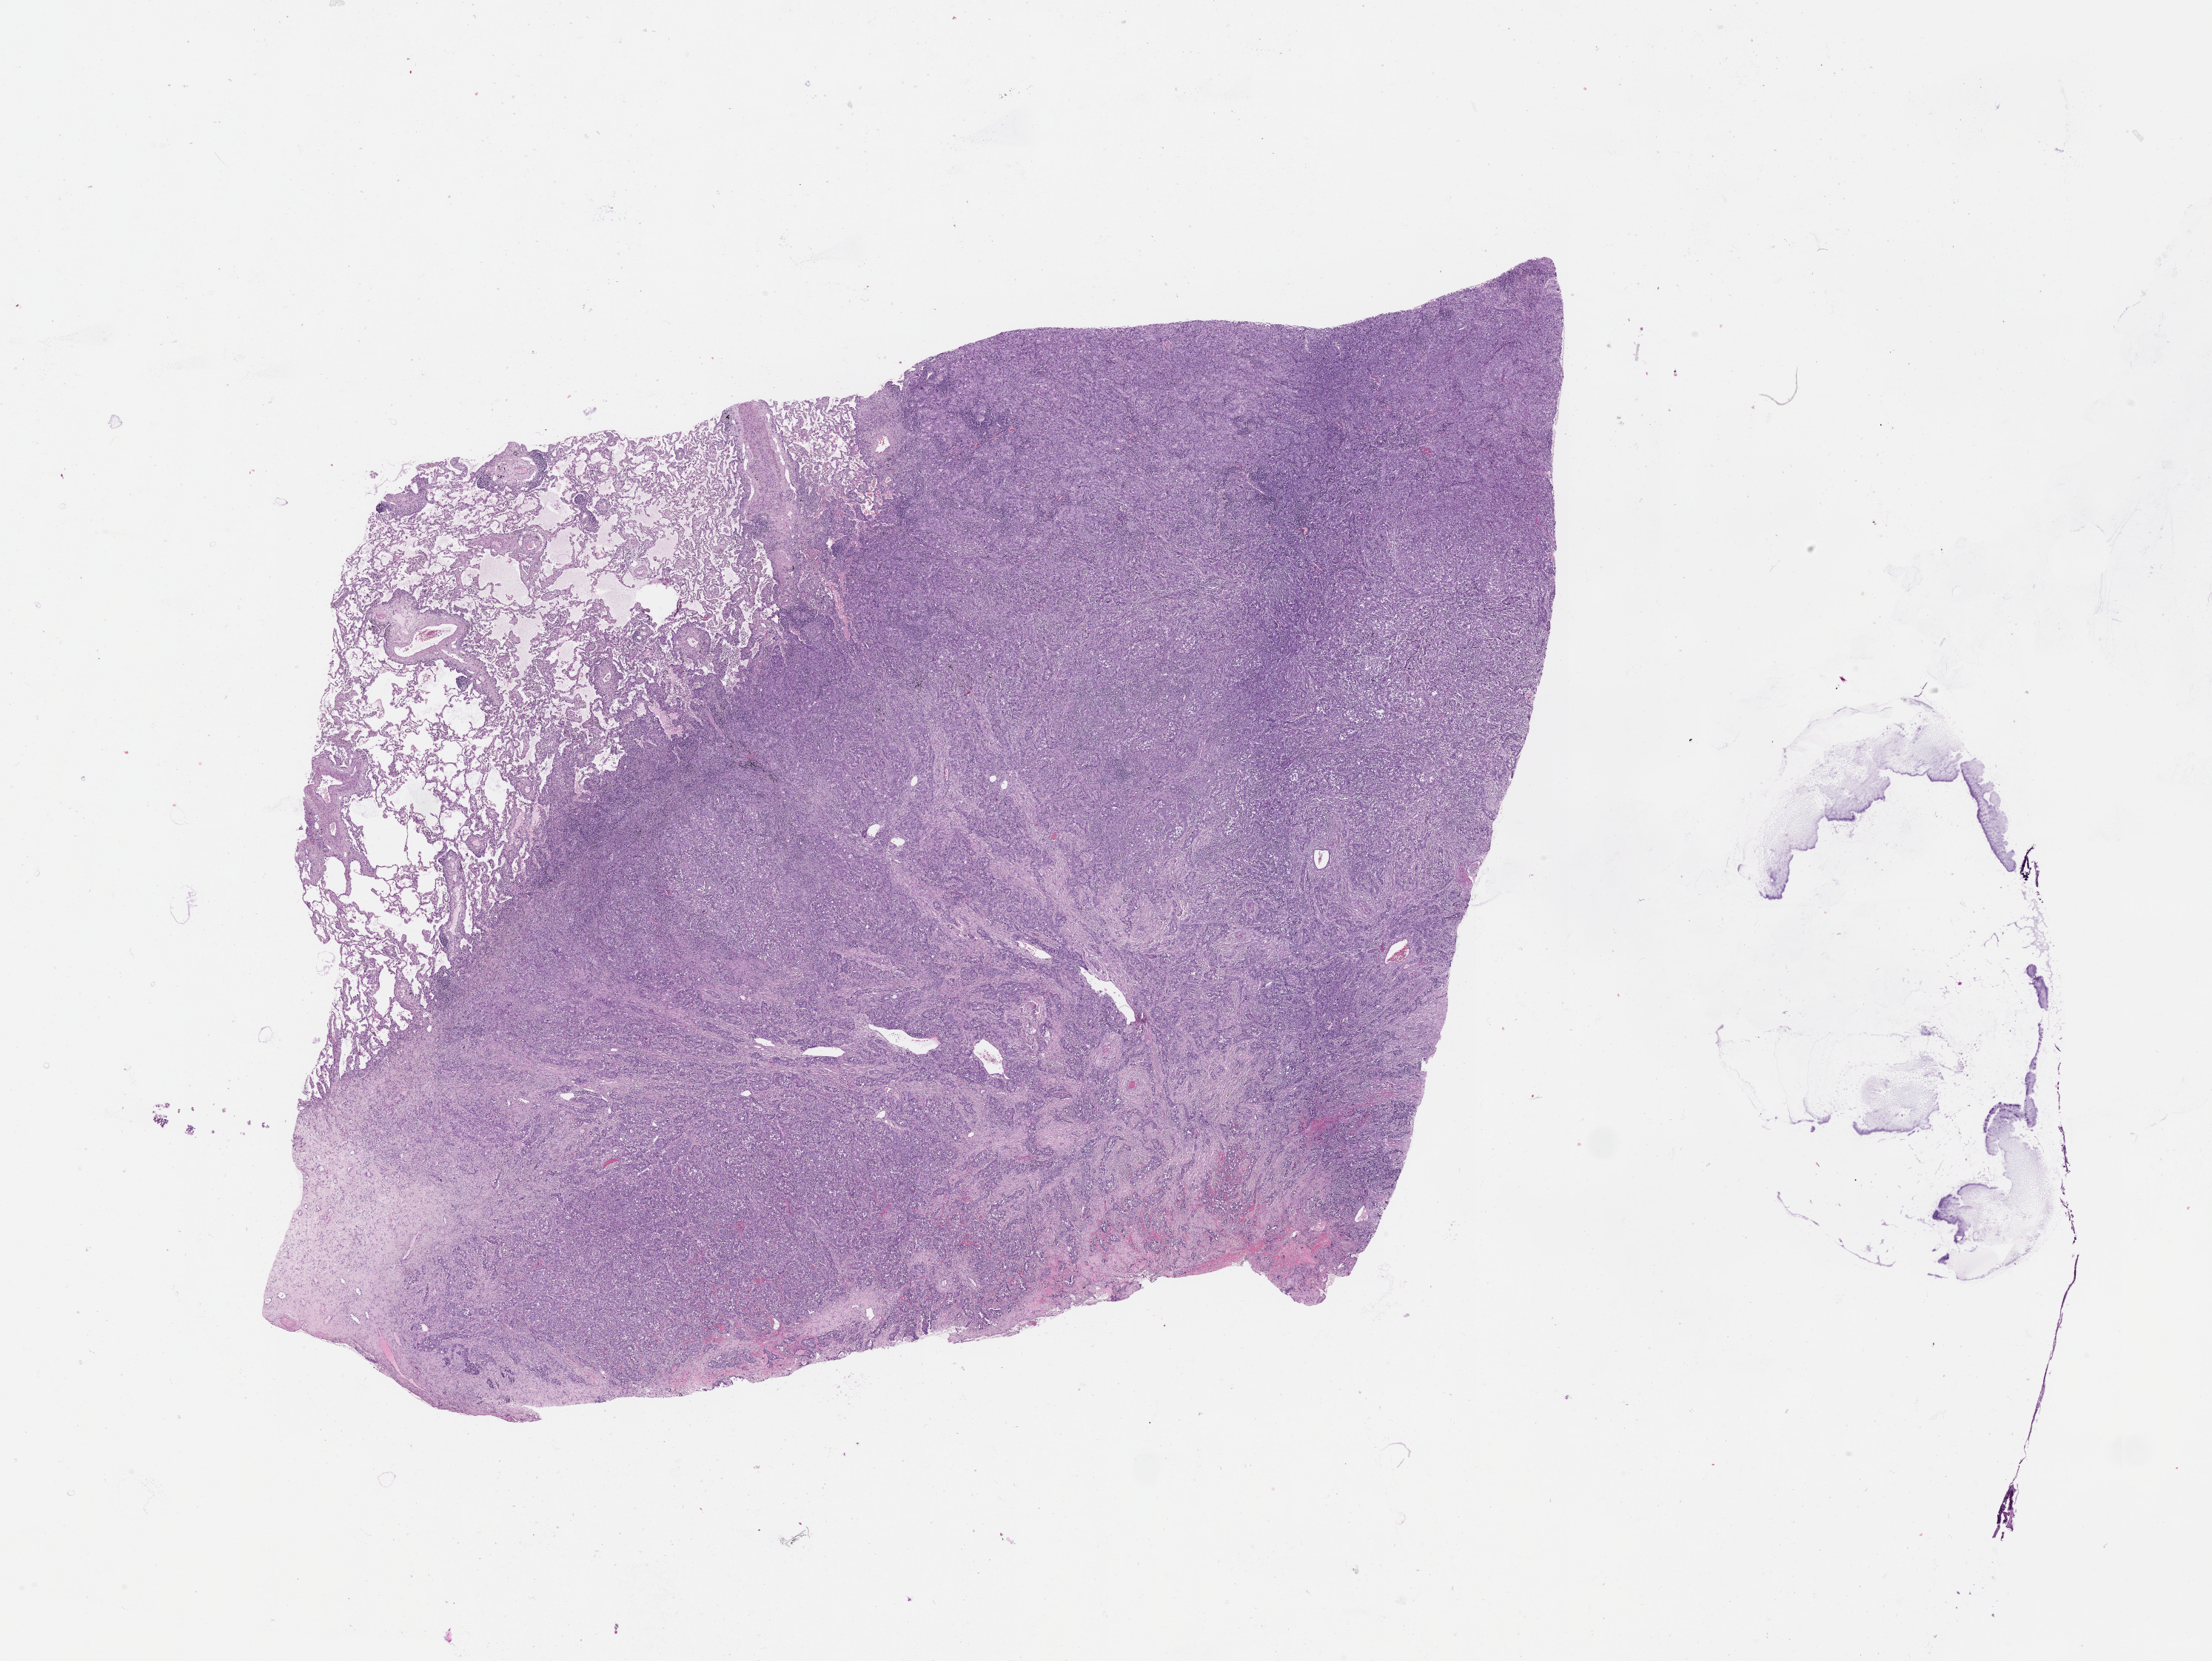
Digitized Hematoxylin and eosin (H&E) stained tissue section (whole slide) — low-resolution overview of the scanned area, about 24.1 x 18.1 mm. Lung, tissue type not recorded.
Patient diagnosis (cohort enrolment): squamous cell carcinoma (lung).